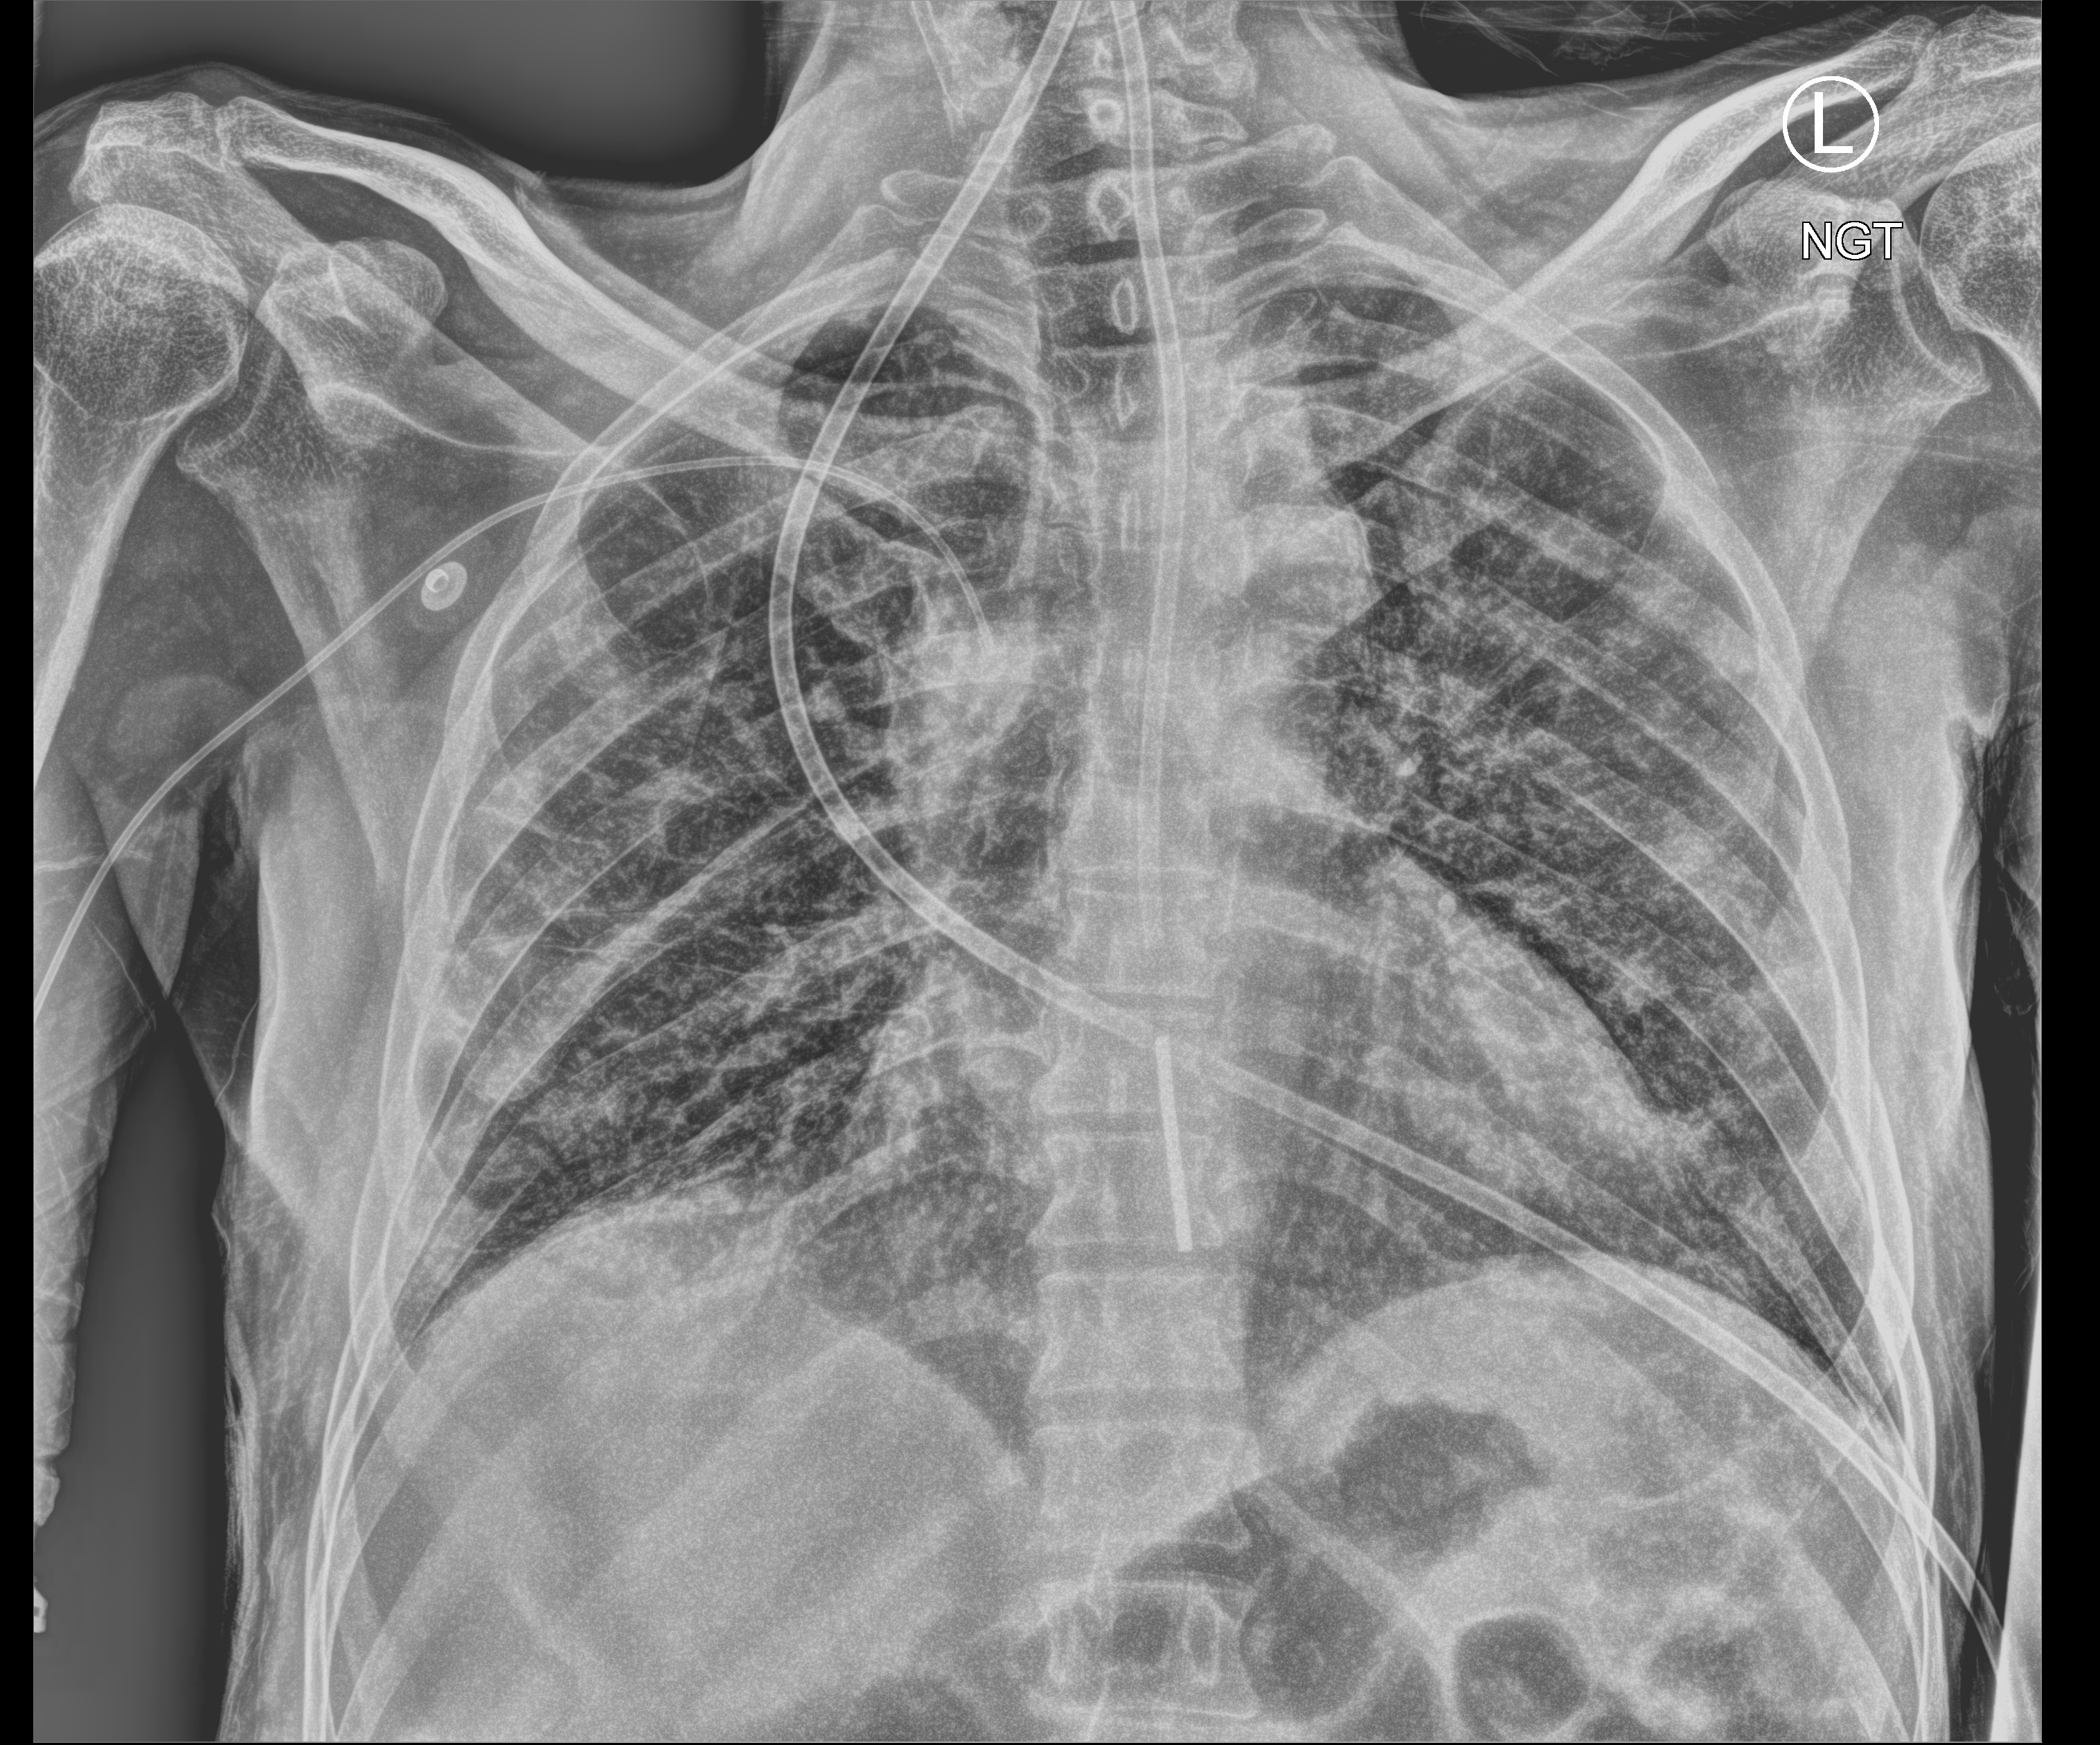
Bedside chest radiograph (computed radiography); anteroposterior (AP) projection. Male patient hospitalised with COVID-19, age 18–59 years.
From the hospital-stay record, not from the radiograph (when in the stay this image was taken is not recorded): hypertension (admission record): no; other chronic lung disease (admission record): no; mechanically ventilated during this hospital stay: yes.